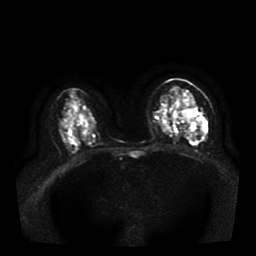
Breast MRI, one axial slice; position 20 of 41 along the scan axis; diffusion-weighted series; image 2 of 4 stored at this slice position (different b-values; order by instance number); 1.5 T; 5 mm slice thickness; 256 × 256 image matrix, field of view 330 × 330 mm. Female patient.
Structures marked on this image (manually delineated by an expert):
- tumour on diffusion-weighted imaging: bounding box [x1, y1, x2, y2] px = [179, 111, 204, 137]